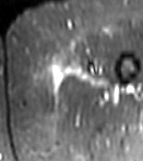
MRI of an extremity soft-tissue mass, one axial slice. Slice 7 of 81 in the series (ordered by position). STIR. MR volume resampled by the dataset authors to the PET/CT grid (not the native acquisition matrix). 143 × 161 image matrix. Female patient. From the clinical record (not read from this slice): histological type: myxofibrosarcoma; grade: intermediate; site of the primary tumour: left thigh.
Outlined on this slice (expert contour drawn on MRI and transferred to this co-registered scan by the dataset authors):
- gross tumour volume including surrounding oedema: bounding box <42,53,107,93> (left, top, right, bottom; pixels)